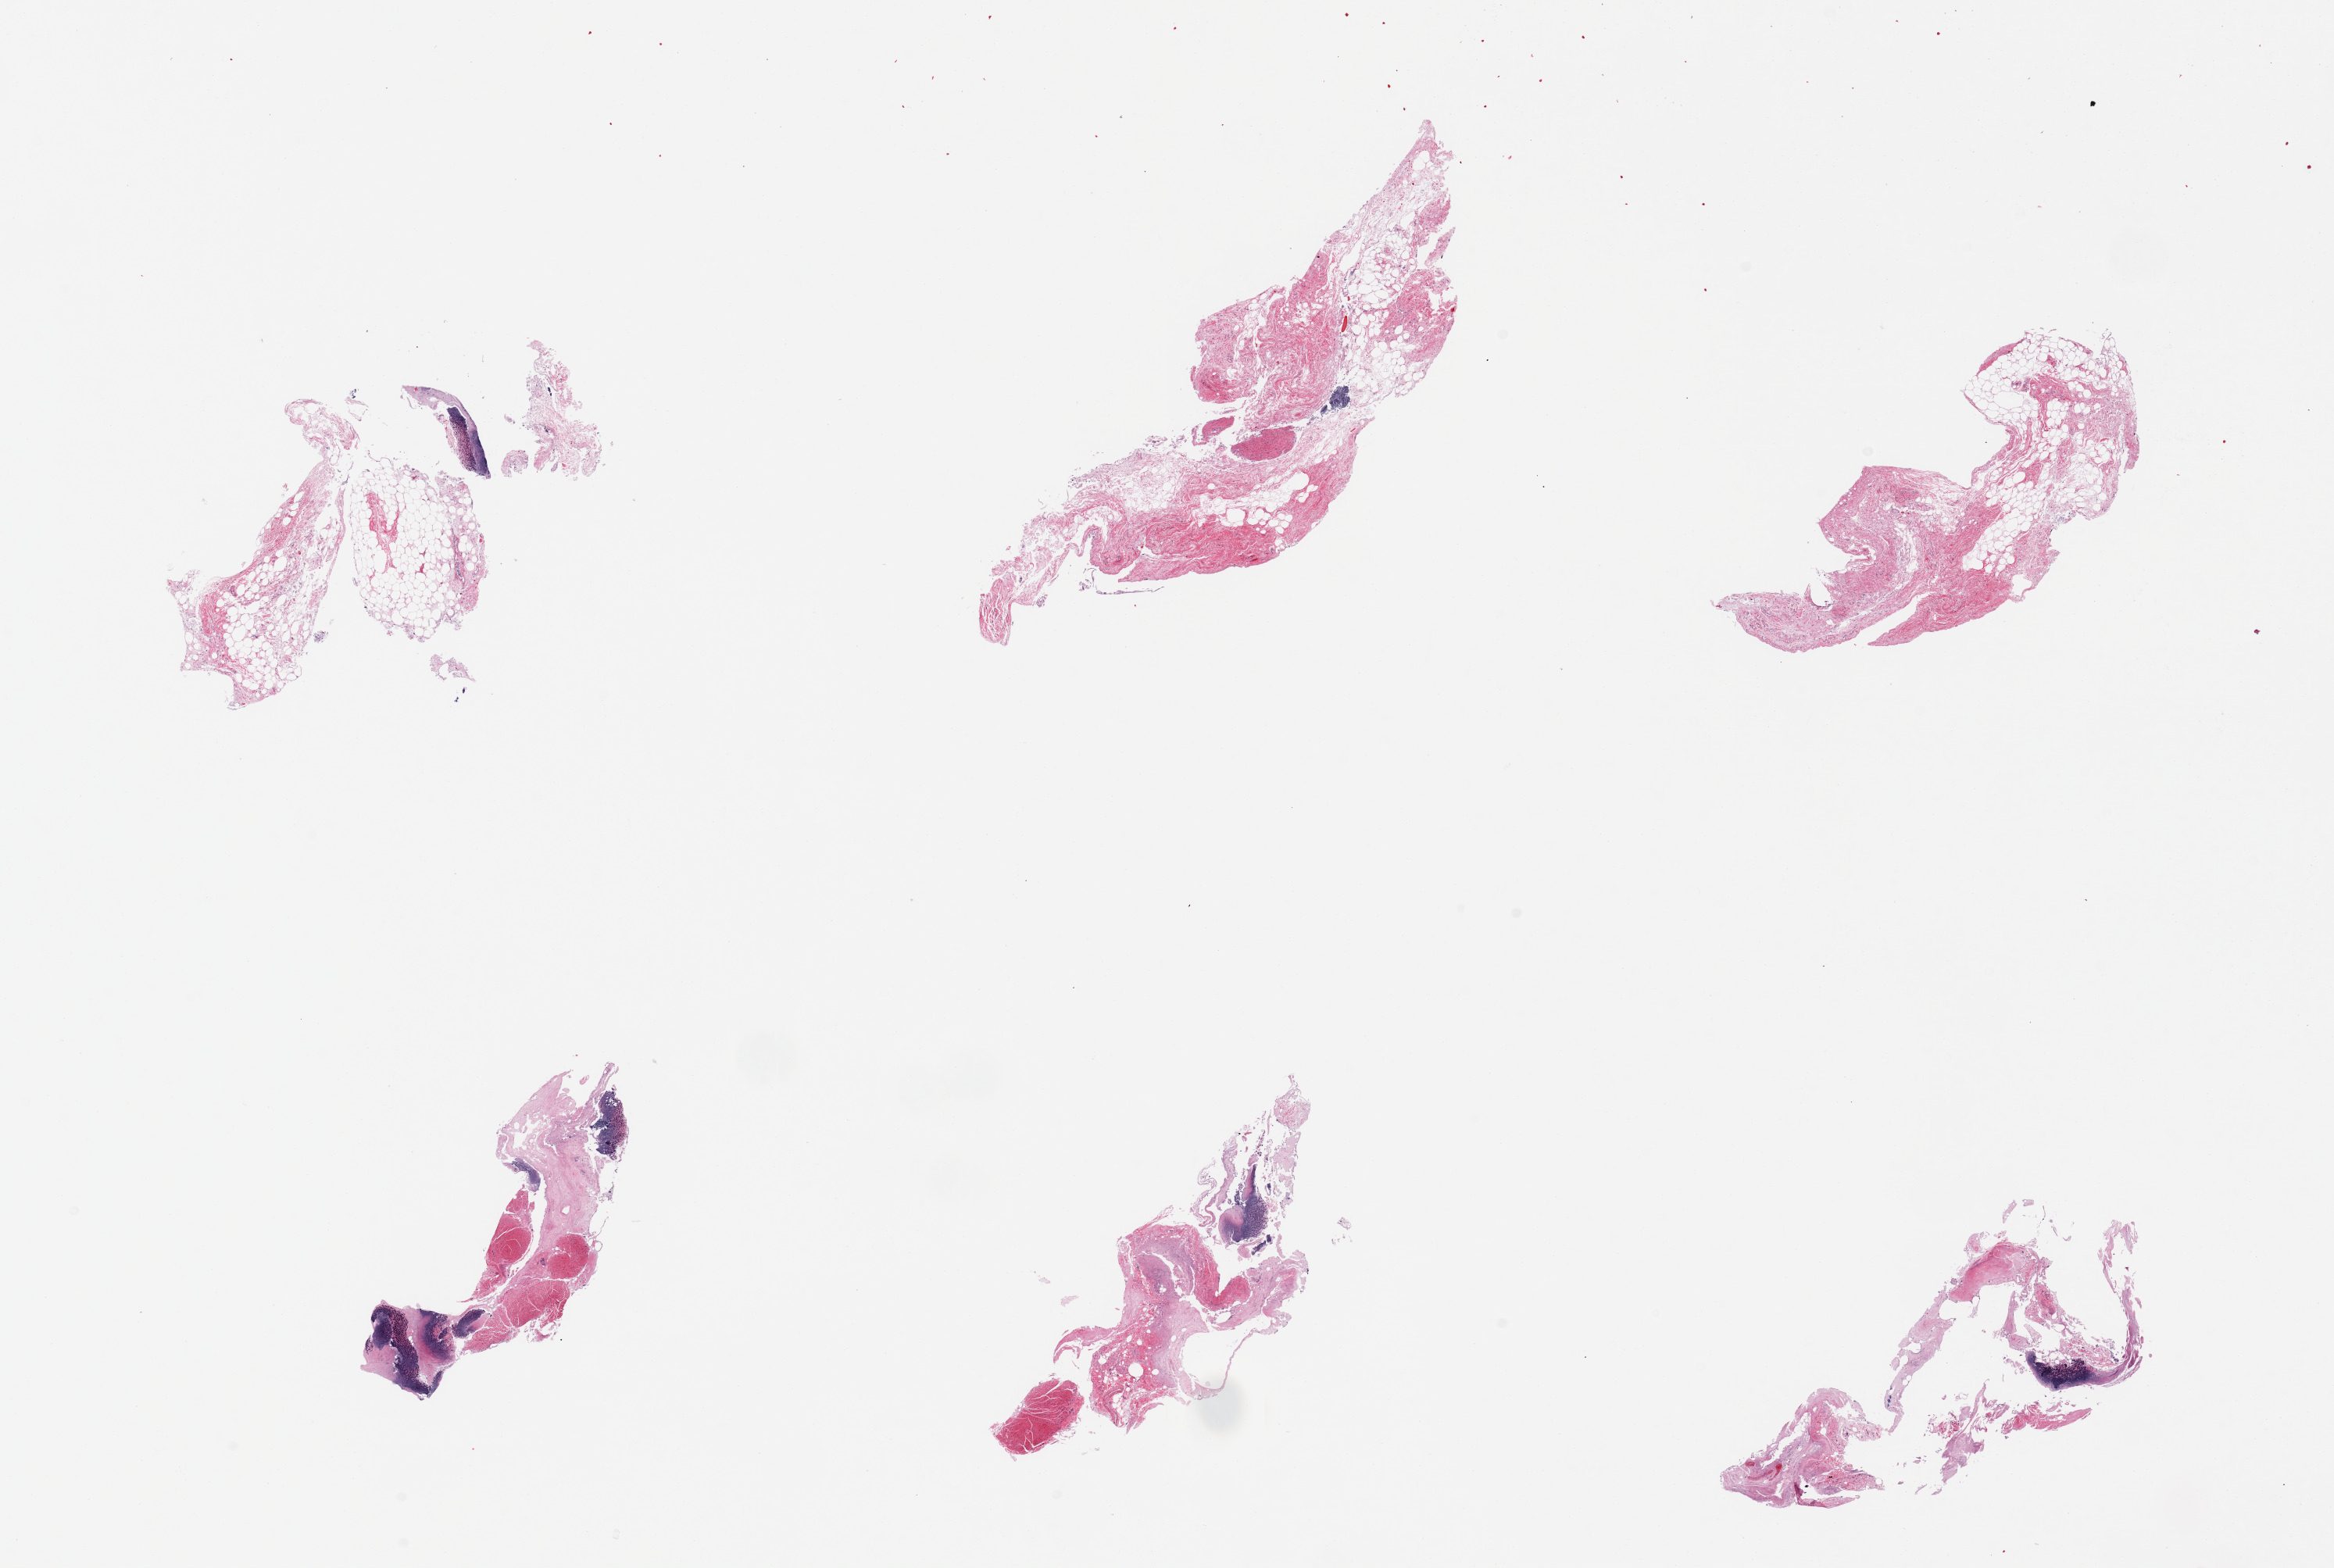
Whole-slide image, H&E stain, whole scanned area (about 23.6 x 15.9 mm, from a 20x scan) shown as a low-resolution overview. PAXgene-fixed paraffin-embedded (PFPE) section. Section of ileum (target tissue). Tissue donor sample. Donor sex: male.
- reviewer comment on this tissue sample: 6 pieces, mucosa largely sloughed, trace lymphoid aggregates